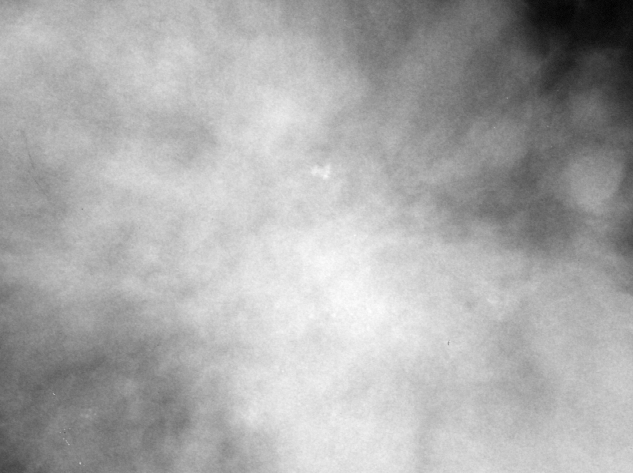
Region of interest cut from a scanned film mammogram (one marked finding); left breast; CC view.
- Calcifications, morphology punctate, distribution clustered; BI-RADS assessment category 4; subtlety rating 2 on a 1 (subtle) to 5 (obvious) scale; pathology result (as recorded, not read from the image): benign.